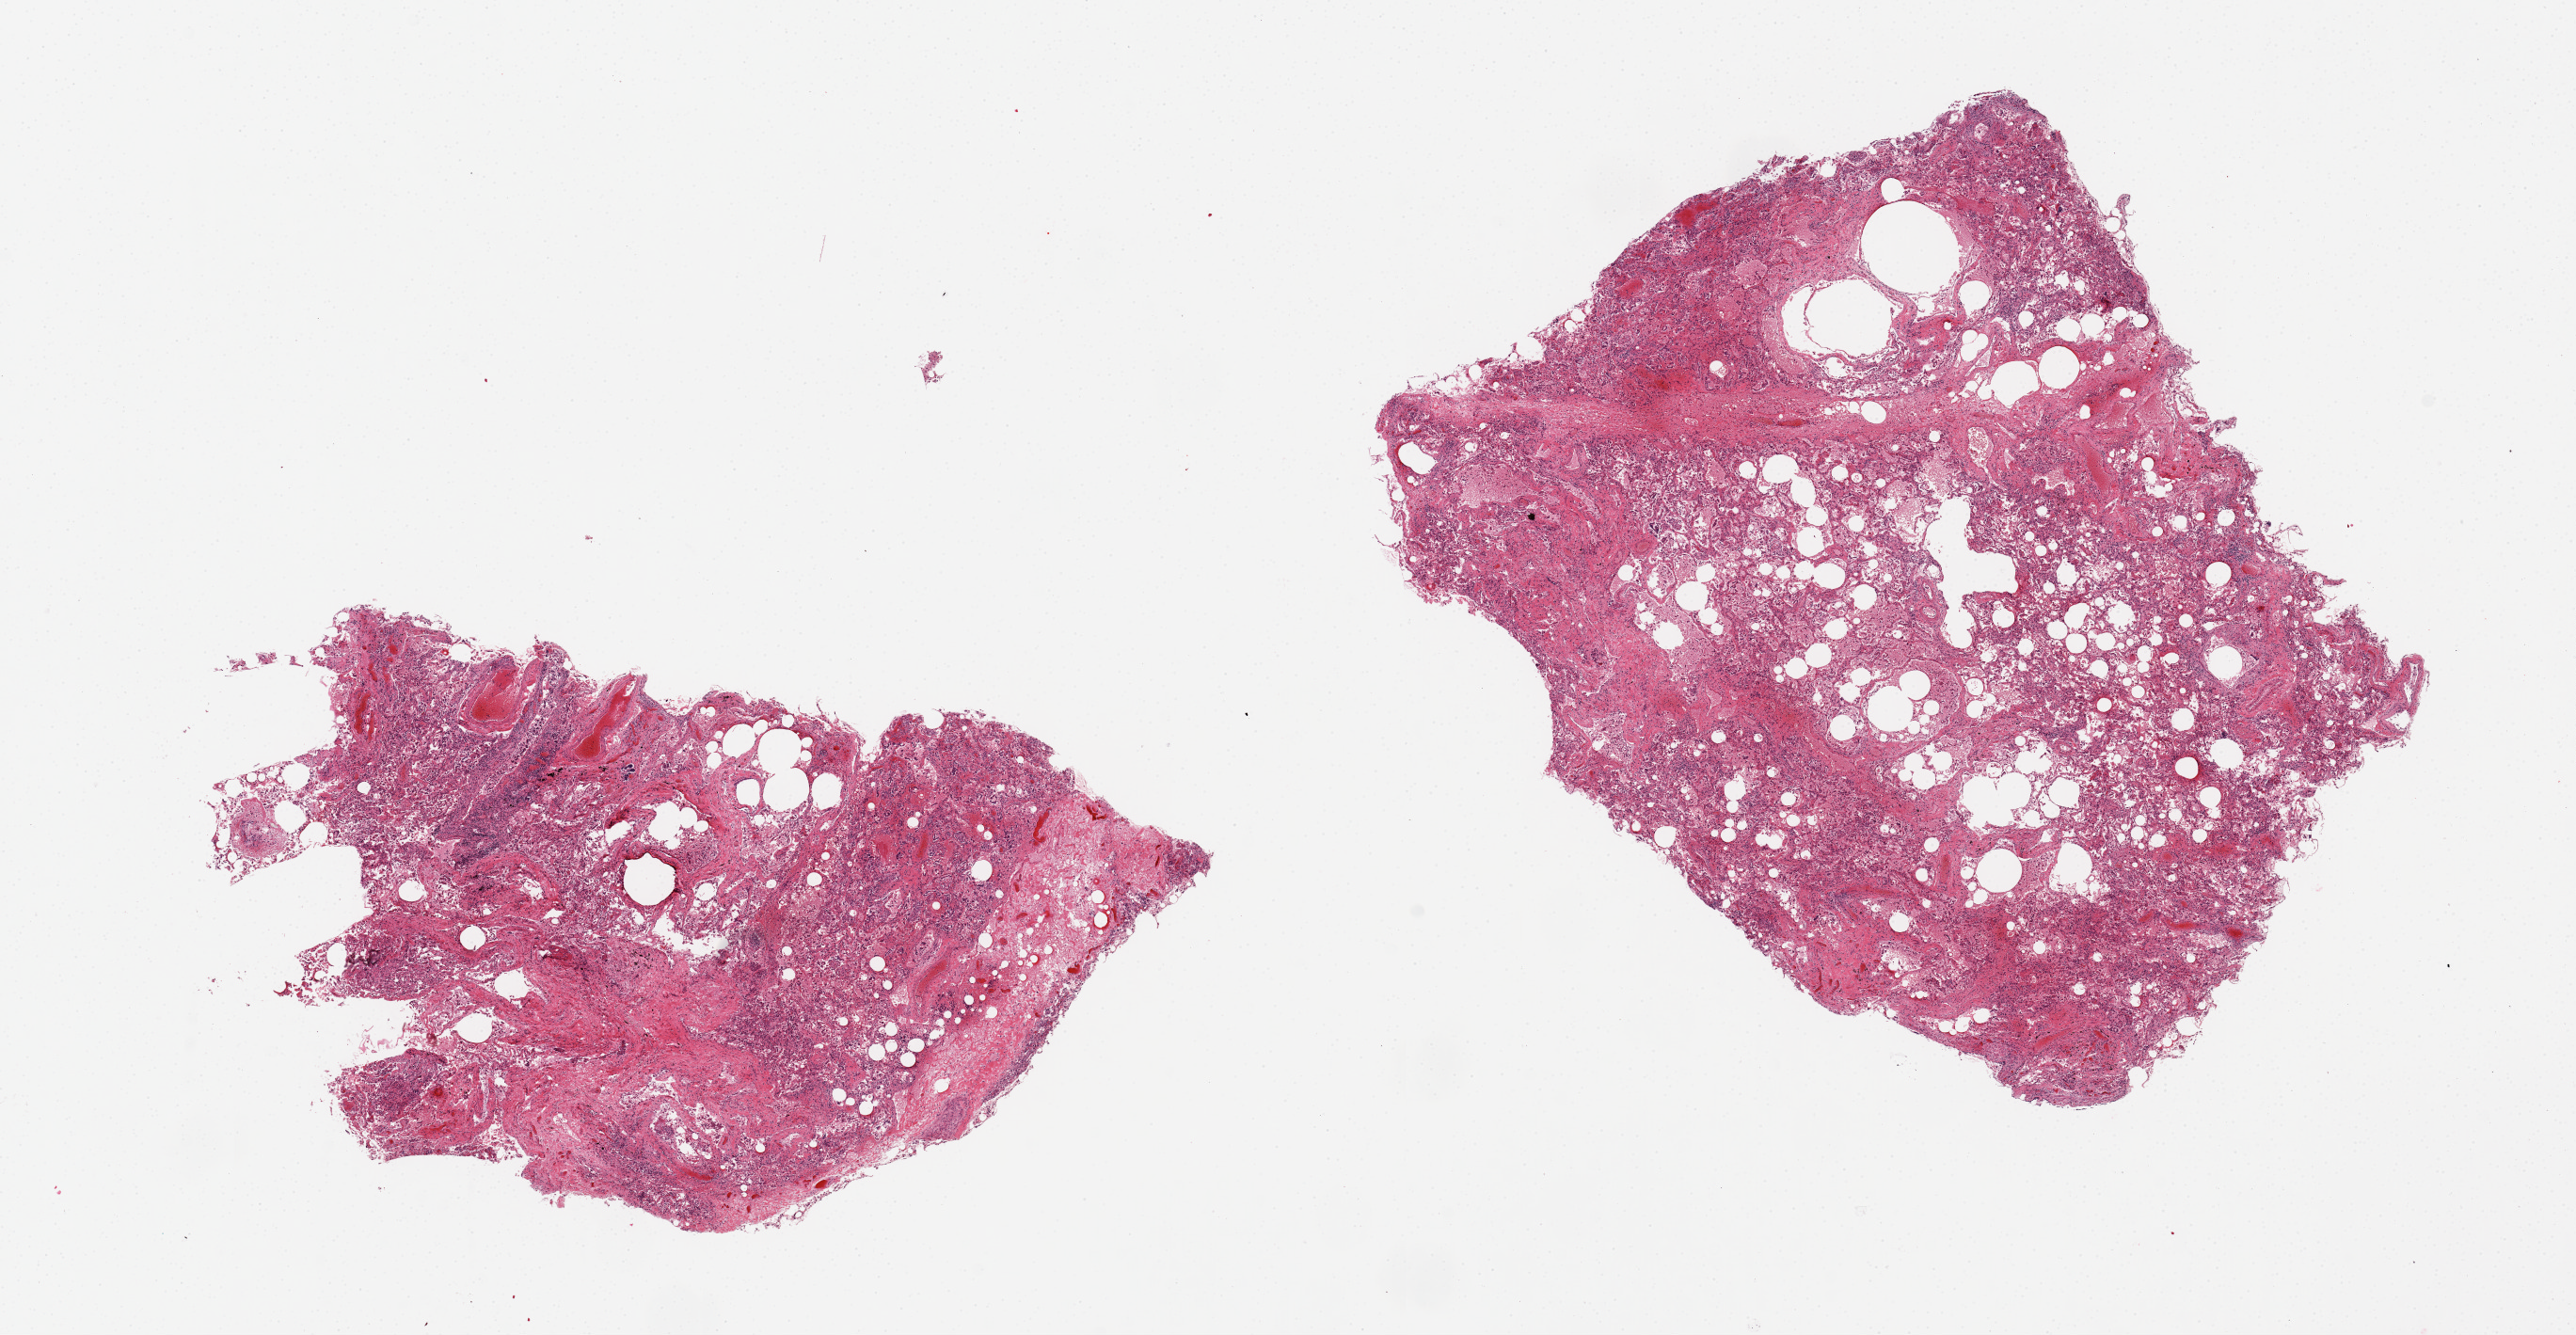
H&E whole-slide image, whole scanned area (about 21.7 x 11.2 mm) shown as a low-resolution overview. PAXgene-fixed paraffin-embedded (PFPE) section. Sampled site (target tissue): lung. Tissue donor sample. Donor: male.
Review note (as recorded): 2 pieces. Extensive alveolar hemorrhage. Emphysema.